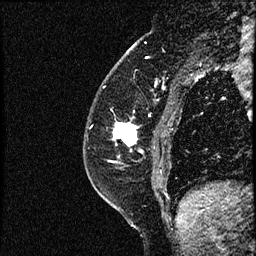
Breast MRI (dynamic contrast-enhanced), one sagittal slice; position 20 of 52 along the scan axis; dynamic contrast-enhanced study with each time point stored as its own series, time point 2 of 3 at this slice position (early post-contrast, ordered by acquisition time); 1.5 T; TE 4.2 ms, TR 17.6 ms; 256 × 256 image matrix, field of view 200 × 200 mm. Female patient, age 49 years. From the clinical record (not read from this slice): setting: breast cancer imaged before/during neoadjuvant chemotherapy; receptor status: HER2-positive.
Annotated regions visible in this slice (semi-automatically segmented with operator editing):
- analysis volume of interest (the breast-tissue region the enhancement analysis was run in; not a lesion): box from (x=85, y=65) to (x=182, y=175) px
- tumour enhancement mask (voxels above the 100 % enhancement threshold inside the analysis volume of interest): (x=115, y=124)–(x=144, y=153)